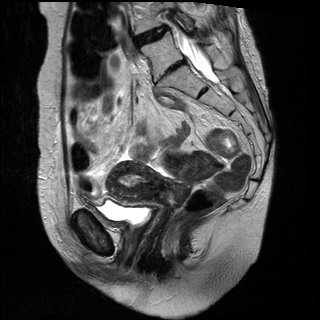
Pelvic MRI for cervical cancer, one sagittal slice; slice 16 of 31 in the series (ordered by position); T2-weighted; 1.5 T; TE 89 ms, TR 3890 ms; 4 mm slice thickness; 320 × 320 image matrix, field of view 260 × 260 mm. Female patient, age 61 years.
Structures marked on this image (outlined manually by an expert reader):
- uterus and cervix: bounding box <106,160,190,209> (left, top, right, bottom; pixels)